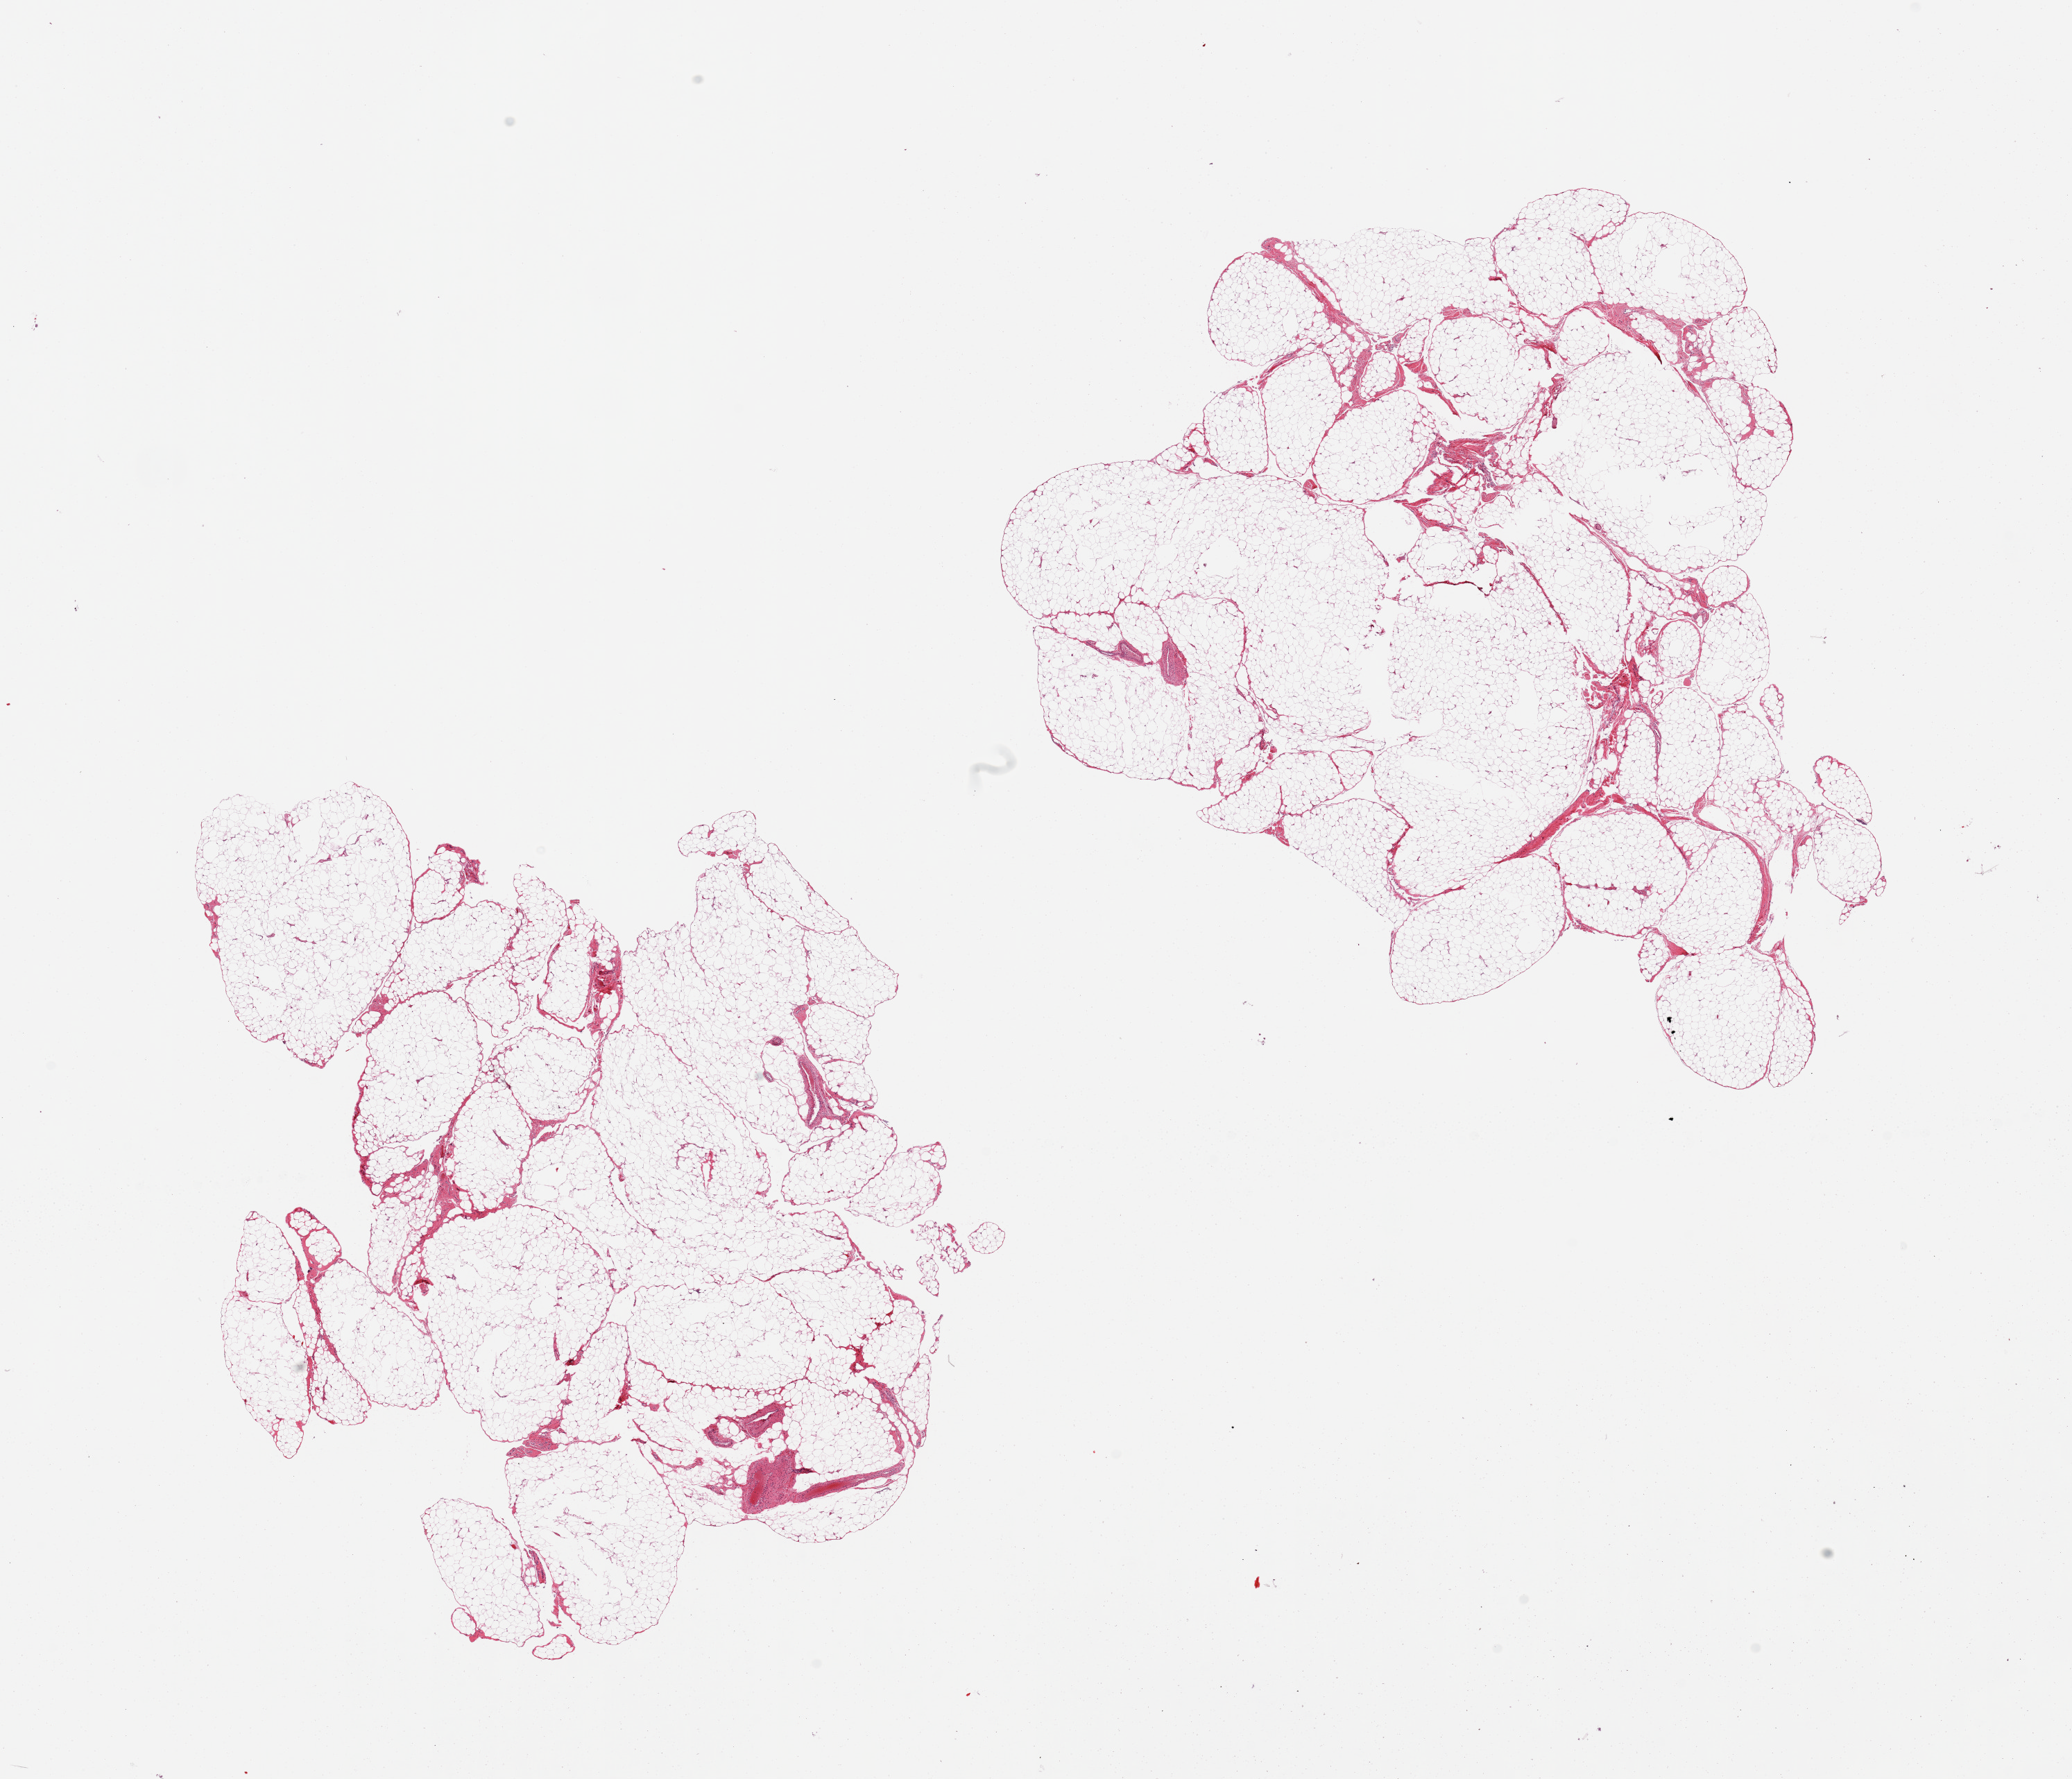
Hematoxylin and eosin (H&E) whole-slide image, brightfield, whole scanned area (about 23.6 x 20.3 mm, from a 20x scan) shown as a low-resolution overview, PAXgene-fixed, paraffin-embedded tissue, section of omentum (target tissue), donor tissue sample. Female donor.
• review note (as recorded): 2 pieces, ~10% vessel/fibrous tissue